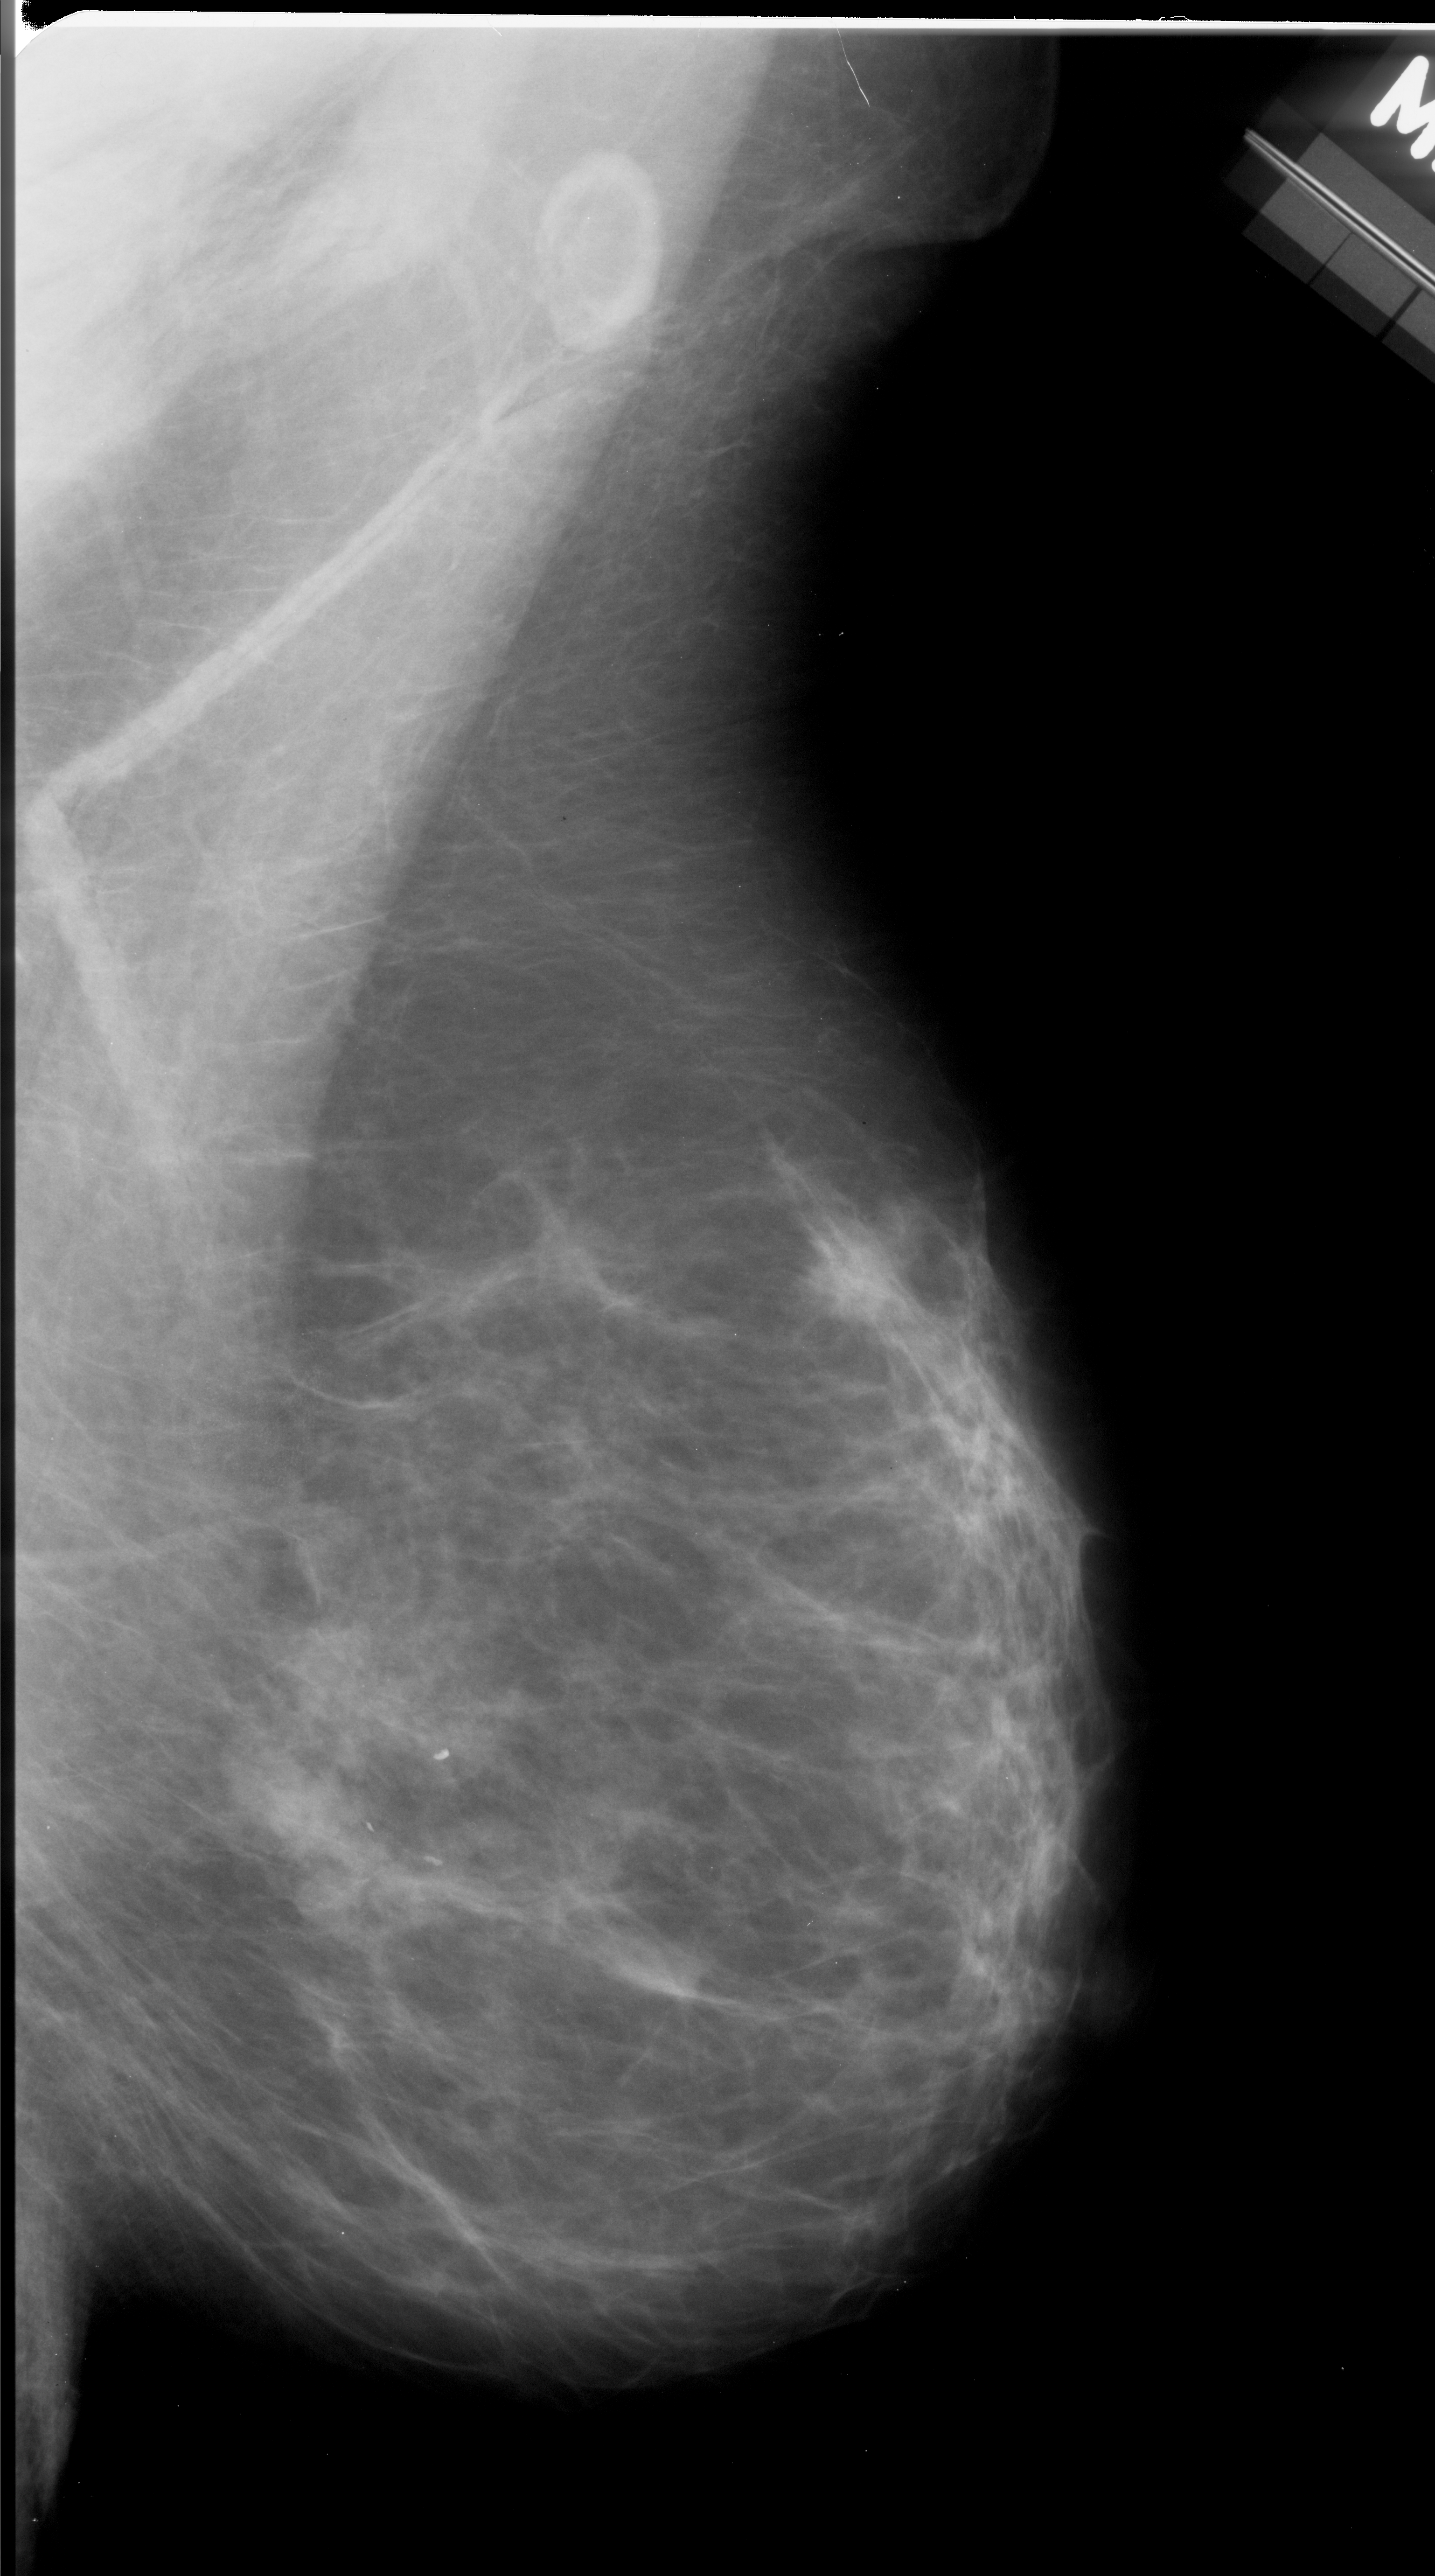
Scanned film-screen mammogram. Right breast. Mediolateral oblique (MLO) view. Breast composition: scattered fibroglandular densities (BI-RADS density category 2 of 4). 1435 × 2576 image matrix.
Marked abnormalities (boxes around the expert regions of interest):
- mass, shape irregular, margins ill defined; BI-RADS assessment category 4; pathology (as recorded): malignant: bounding box <198,1727,370,1872> (left, top, right, bottom; pixels)